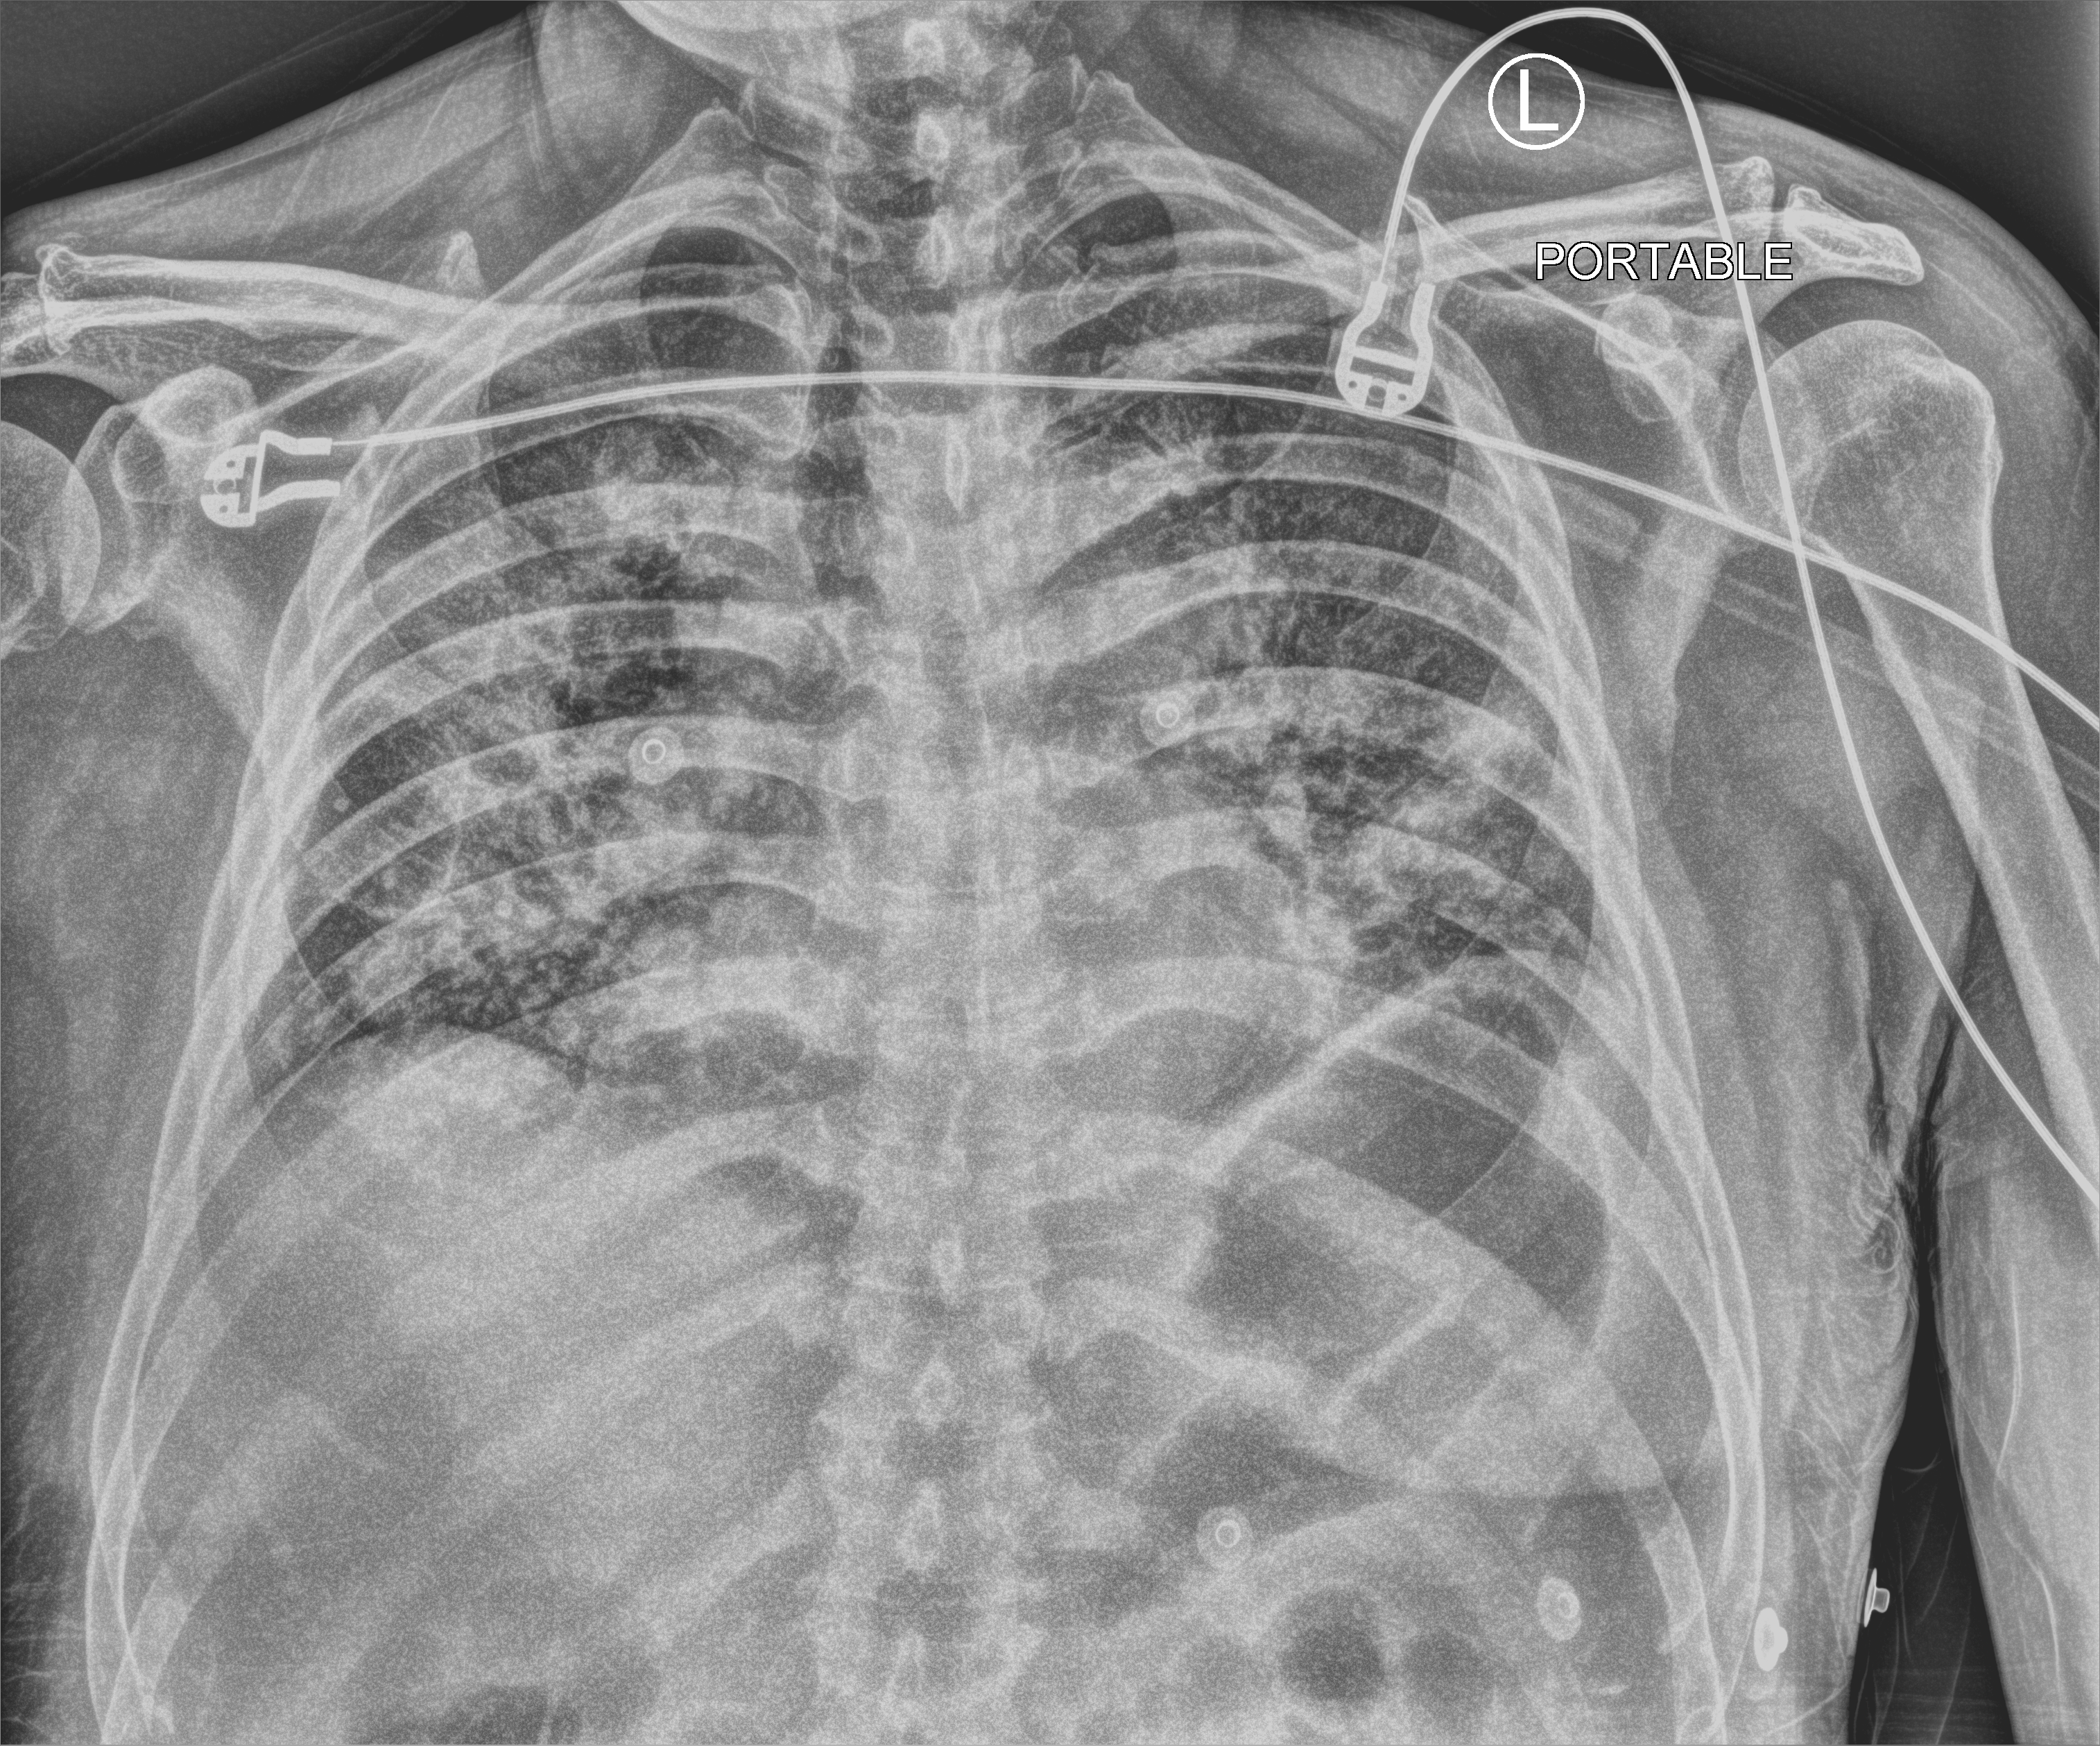
Bedside chest radiograph (computed radiography), anteroposterior (AP) projection. Patient hospitalised with COVID-19; male, aged 60–74 years.
Hospital-stay facts (about this admission, not read from this image; timing relative to this image not recorded): admitted to intensive care during this hospital stay: yes; mechanically ventilated during this hospital stay: yes; length of hospital stay: 28 days.